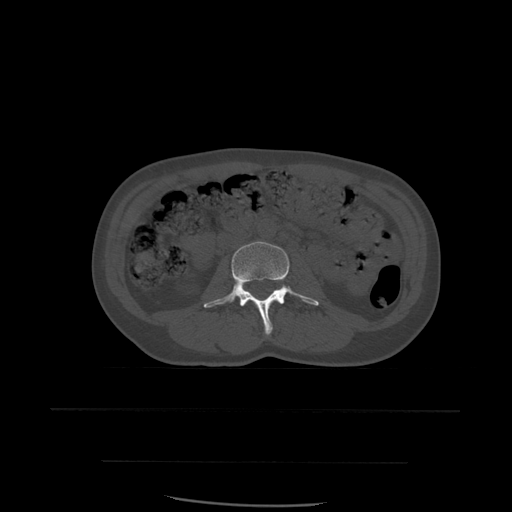
CT including the spine, one axial slice. Slice 198 of 574 in the series (ordered by position). Bone window (W 1800 / L 400 HU). 1.25 mm slice thickness. 512 × 512 image matrix. Patient age 48 years. Case-level facts recorded for this patient, not image findings: primary cancer: lung; vertebrae with lytic lesions (as recorded): T11.
Outlined on this slice (semi-automatically segmented with operator editing):
- L3 vertebra: bounding box [x1, y1, x2, y2] px = [204, 241, 320, 335]